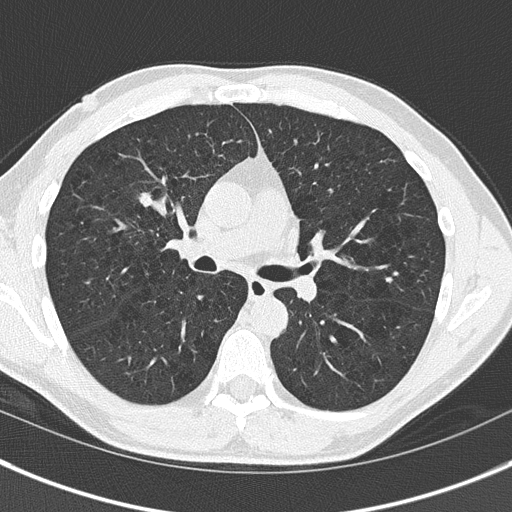
Axial slice from a low-dose chest CT screening exam. Baseline annual screen. Lung window (W 1500 / L -600 HU). 2 mm slice thickness. 512 × 512 image matrix. Male participant, aged 56 years at enrolment.
Lesion marked by an expert reader, bounding box (x1, y1, x2, y2) in pixels: (132, 186, 164, 219). The screening reader recorded 3 non-calcified nodules or masses ≥4 mm on this exam; which of them this box marks is not recorded. Official screen result: positive, change unspecified: nodule(s) >= 4 mm or enlarging nodule(s), mass(es), or other non-specific abnormalities suspicious for lung cancer. Participant outcome: lung cancer diagnosed 228 days after this screen — non-small cell carcinoma, right upper lobe, stage IIIA (AJCC 6th edition), 21 mm at pathology.